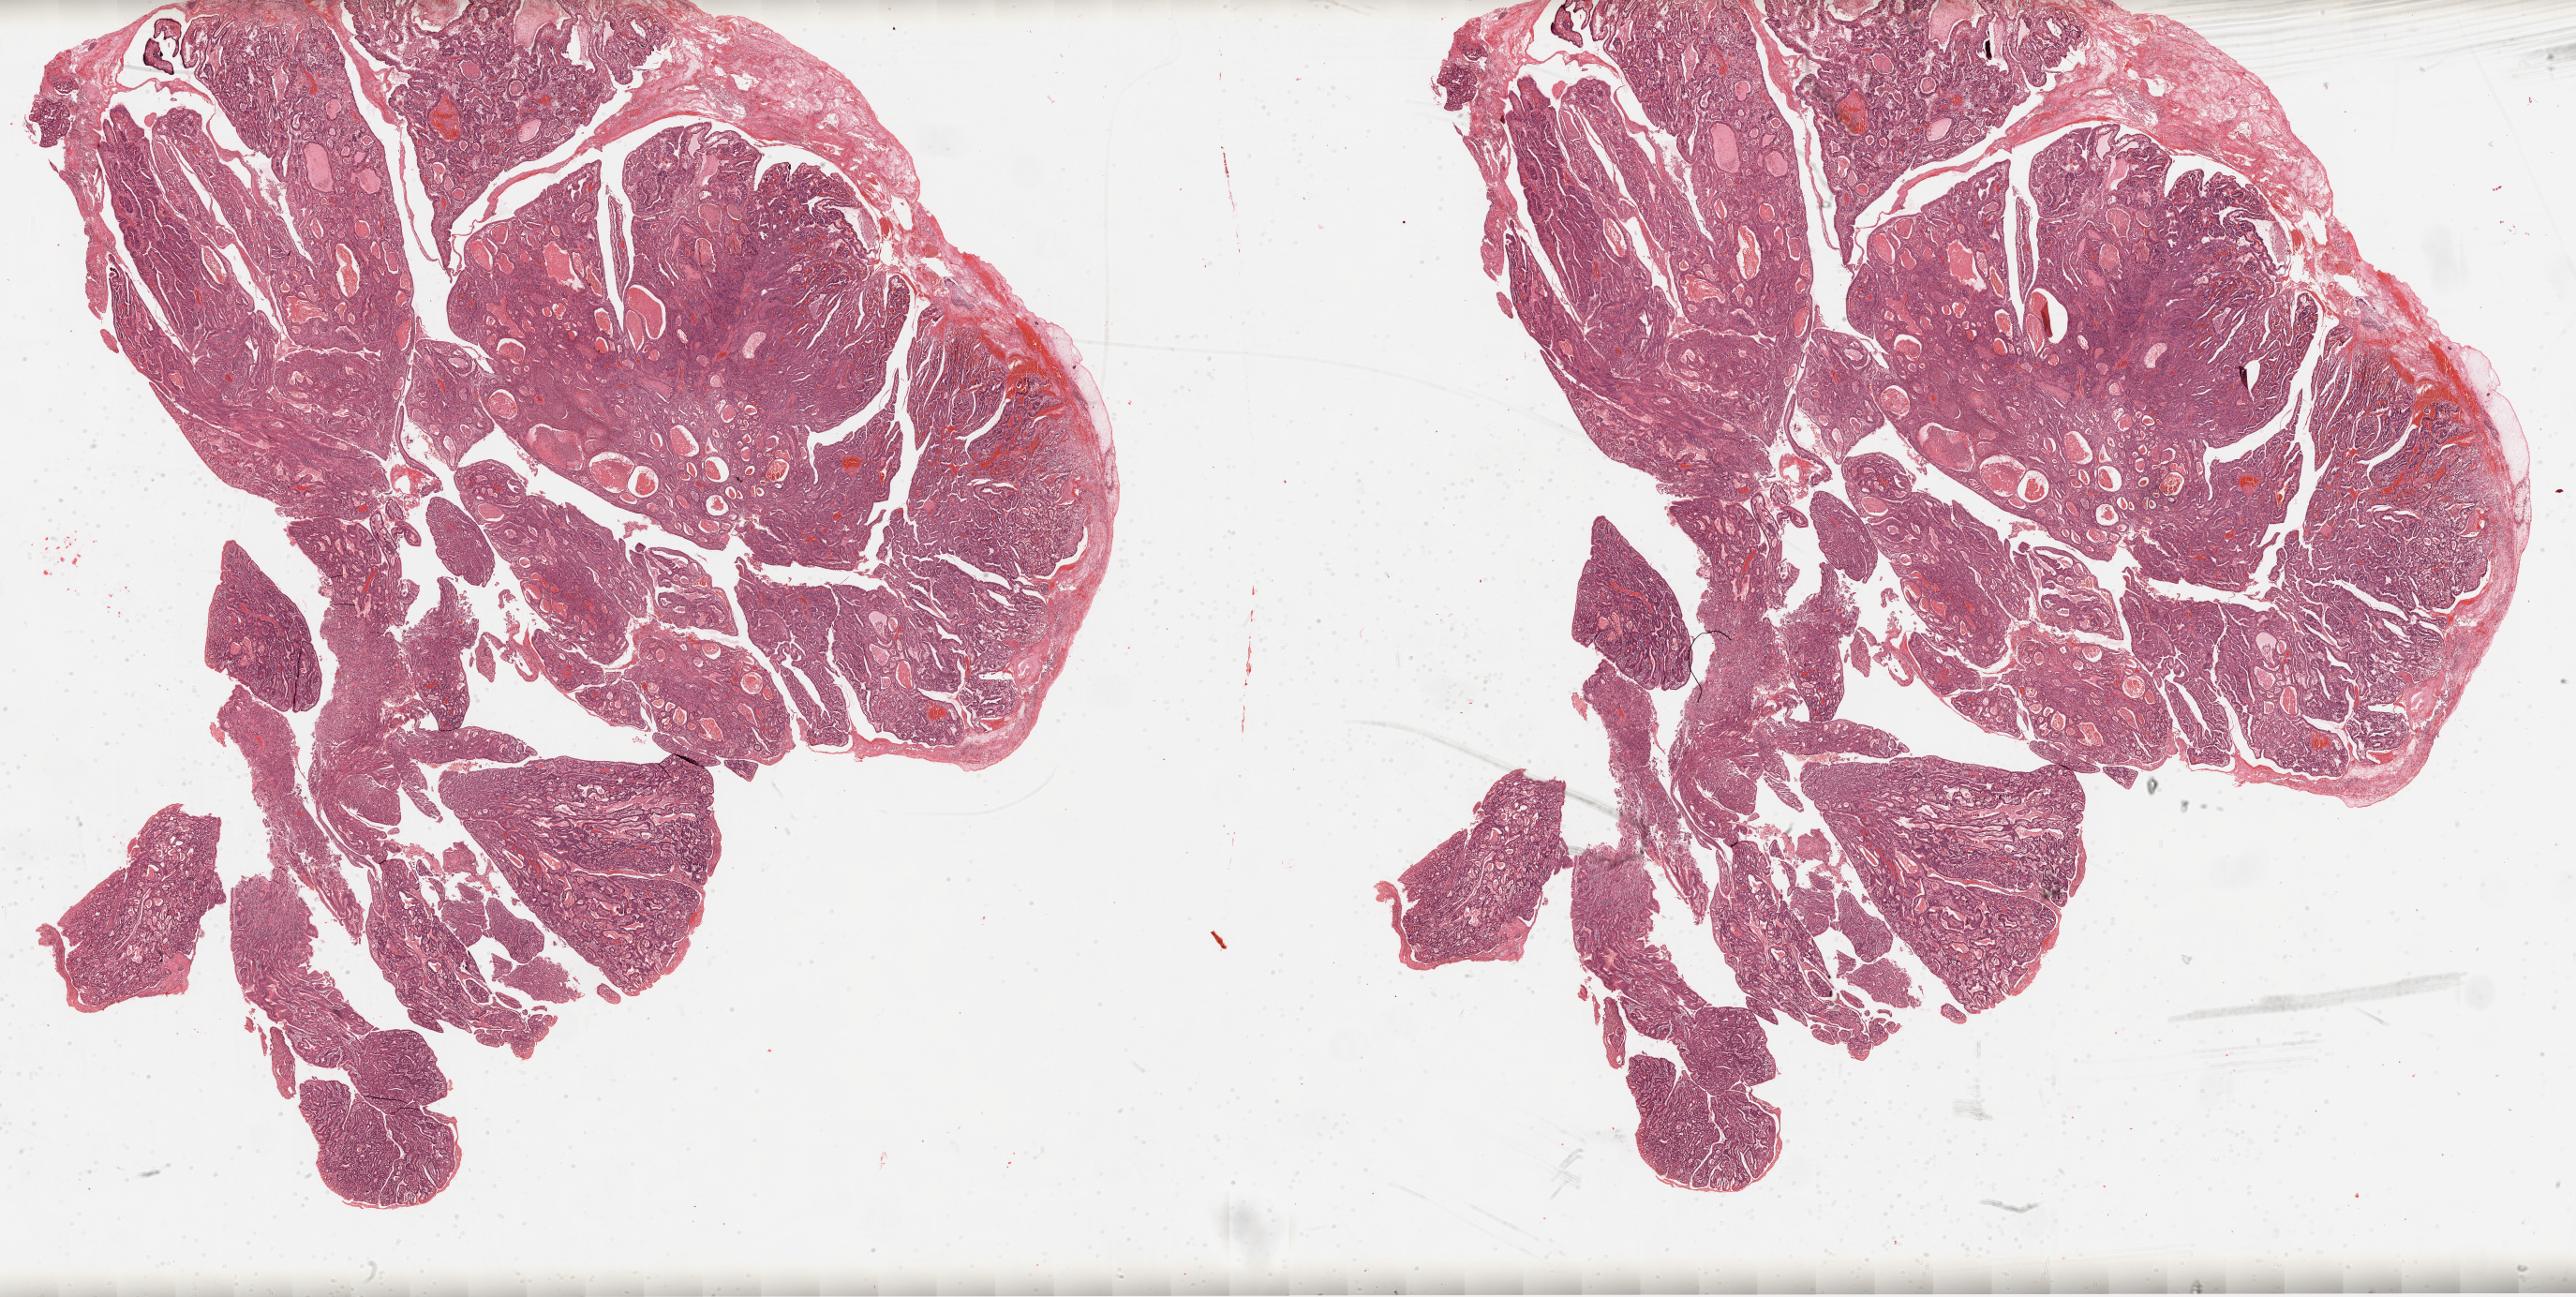
Whole-slide histology image, H&E, shown as a low-resolution overview of the whole scanned area (about 44.0 x 22.1 mm, acquisition: 20x scan); FFPE section; primary tumour sample from the stomach. Patient: male, age at initial diagnosis 56 years. Histologic grade: G3 (poorly differentiated).
- lymph nodes positive (case pathology): 9 of 17 examined
- histologic diagnosis: Adenocarcinoma, intestinal type
- AJCC pathologic stage: IIIB (6th edition)